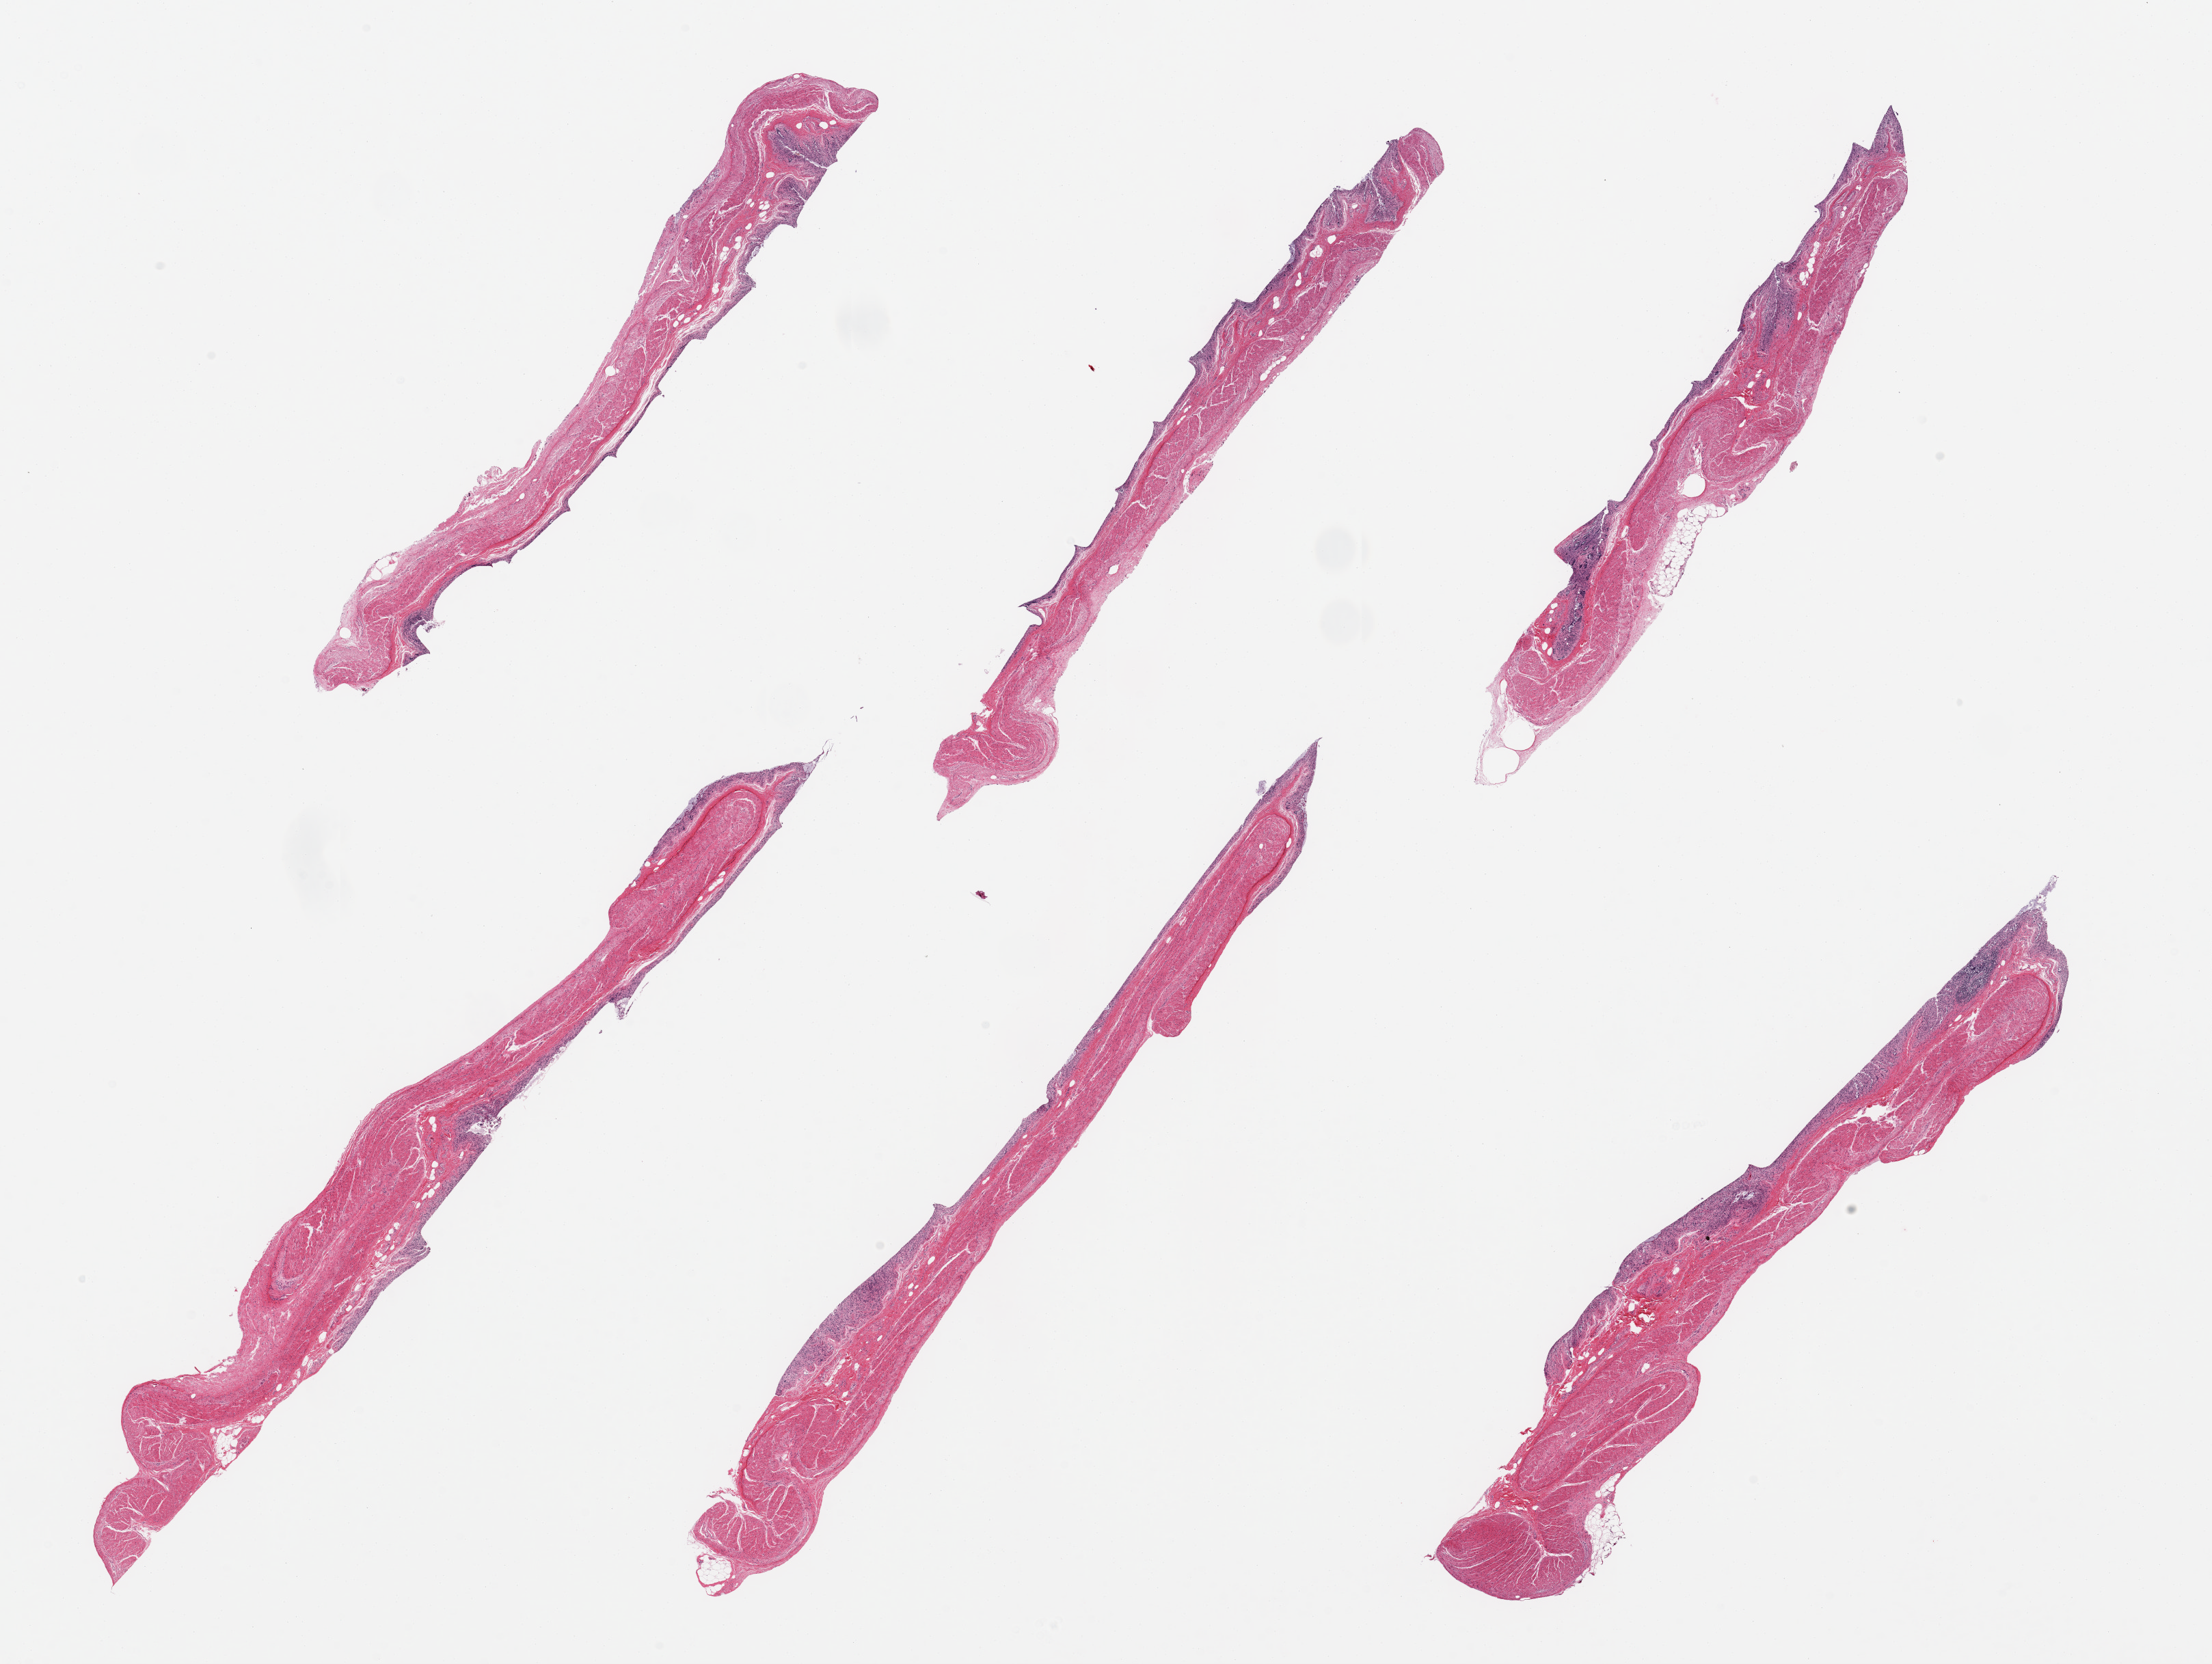
H&E whole-slide image — low-resolution overview of the scanned area, about 25.6 x 19.3 mm. PAXgene-fixed, paraffin-embedded tissue. Target tissue: transverse colon. Donor tissue sample. Donor: male.
Reviewer comment on this tissue sample: 6 pieces; severly autolyzed colonic mucosa and mildly to moderately autolyzed muscularis.